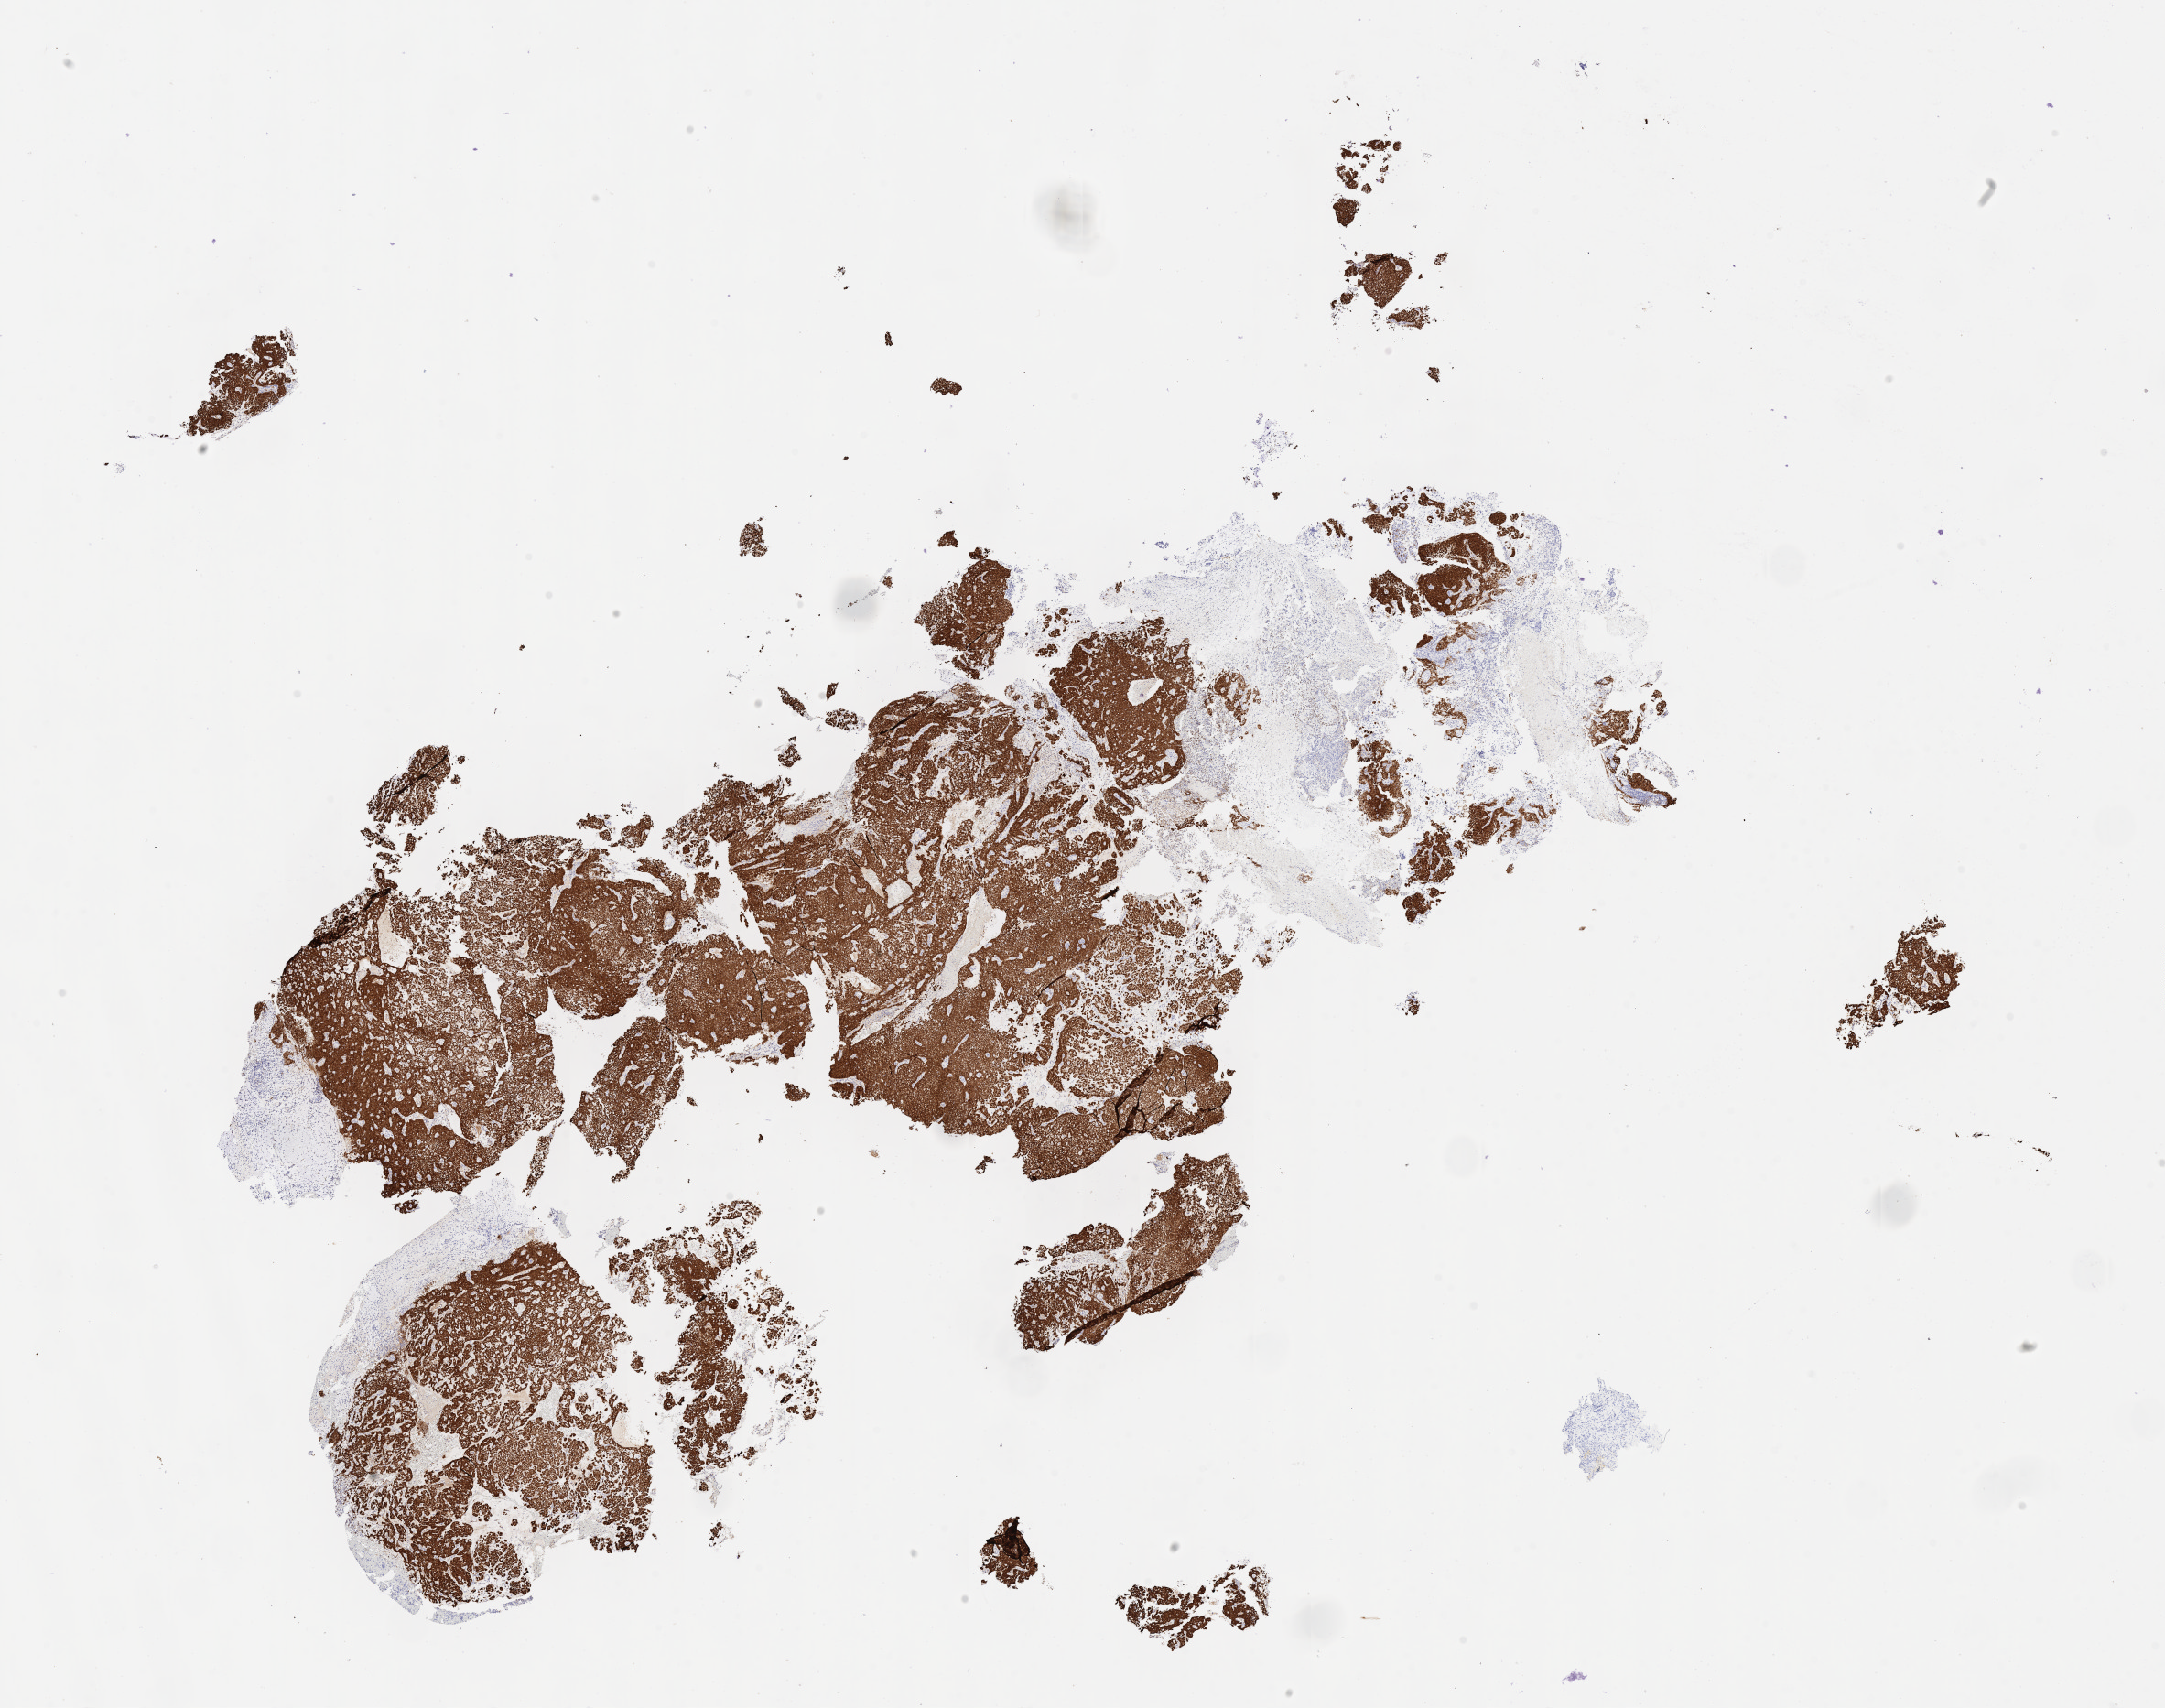
IHC for p16 (p16INK4a), whole-slide image, shown as a low-resolution overview of the whole scanned area (about 19.1 x 15.1 mm), tumor tissue, site: cervix. Female patient, 47 years old.
* diagnosis: Adenocarcinoma, NOS